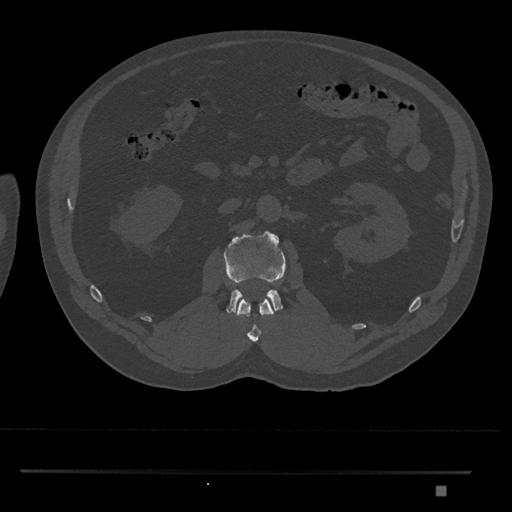
CT including the spine, one axial slice. Position 783 of 1134 along the scan axis. Reconstruction kernel Br40s/3. Bone window (W 1800 / L 400 HU). 512 × 512 image matrix, field of view 429 × 429 mm. Male patient, age 65 years. From the clinical record (not read from this slice): primary cancer: prostate.
Annotated regions visible in this slice (semi-automatic segmentation, software-assisted and operator-edited):
- L1 vertebra: bounding box <237,297,275,342> (left, top, right, bottom; pixels)
- L2 vertebra: <223,231,286,315>